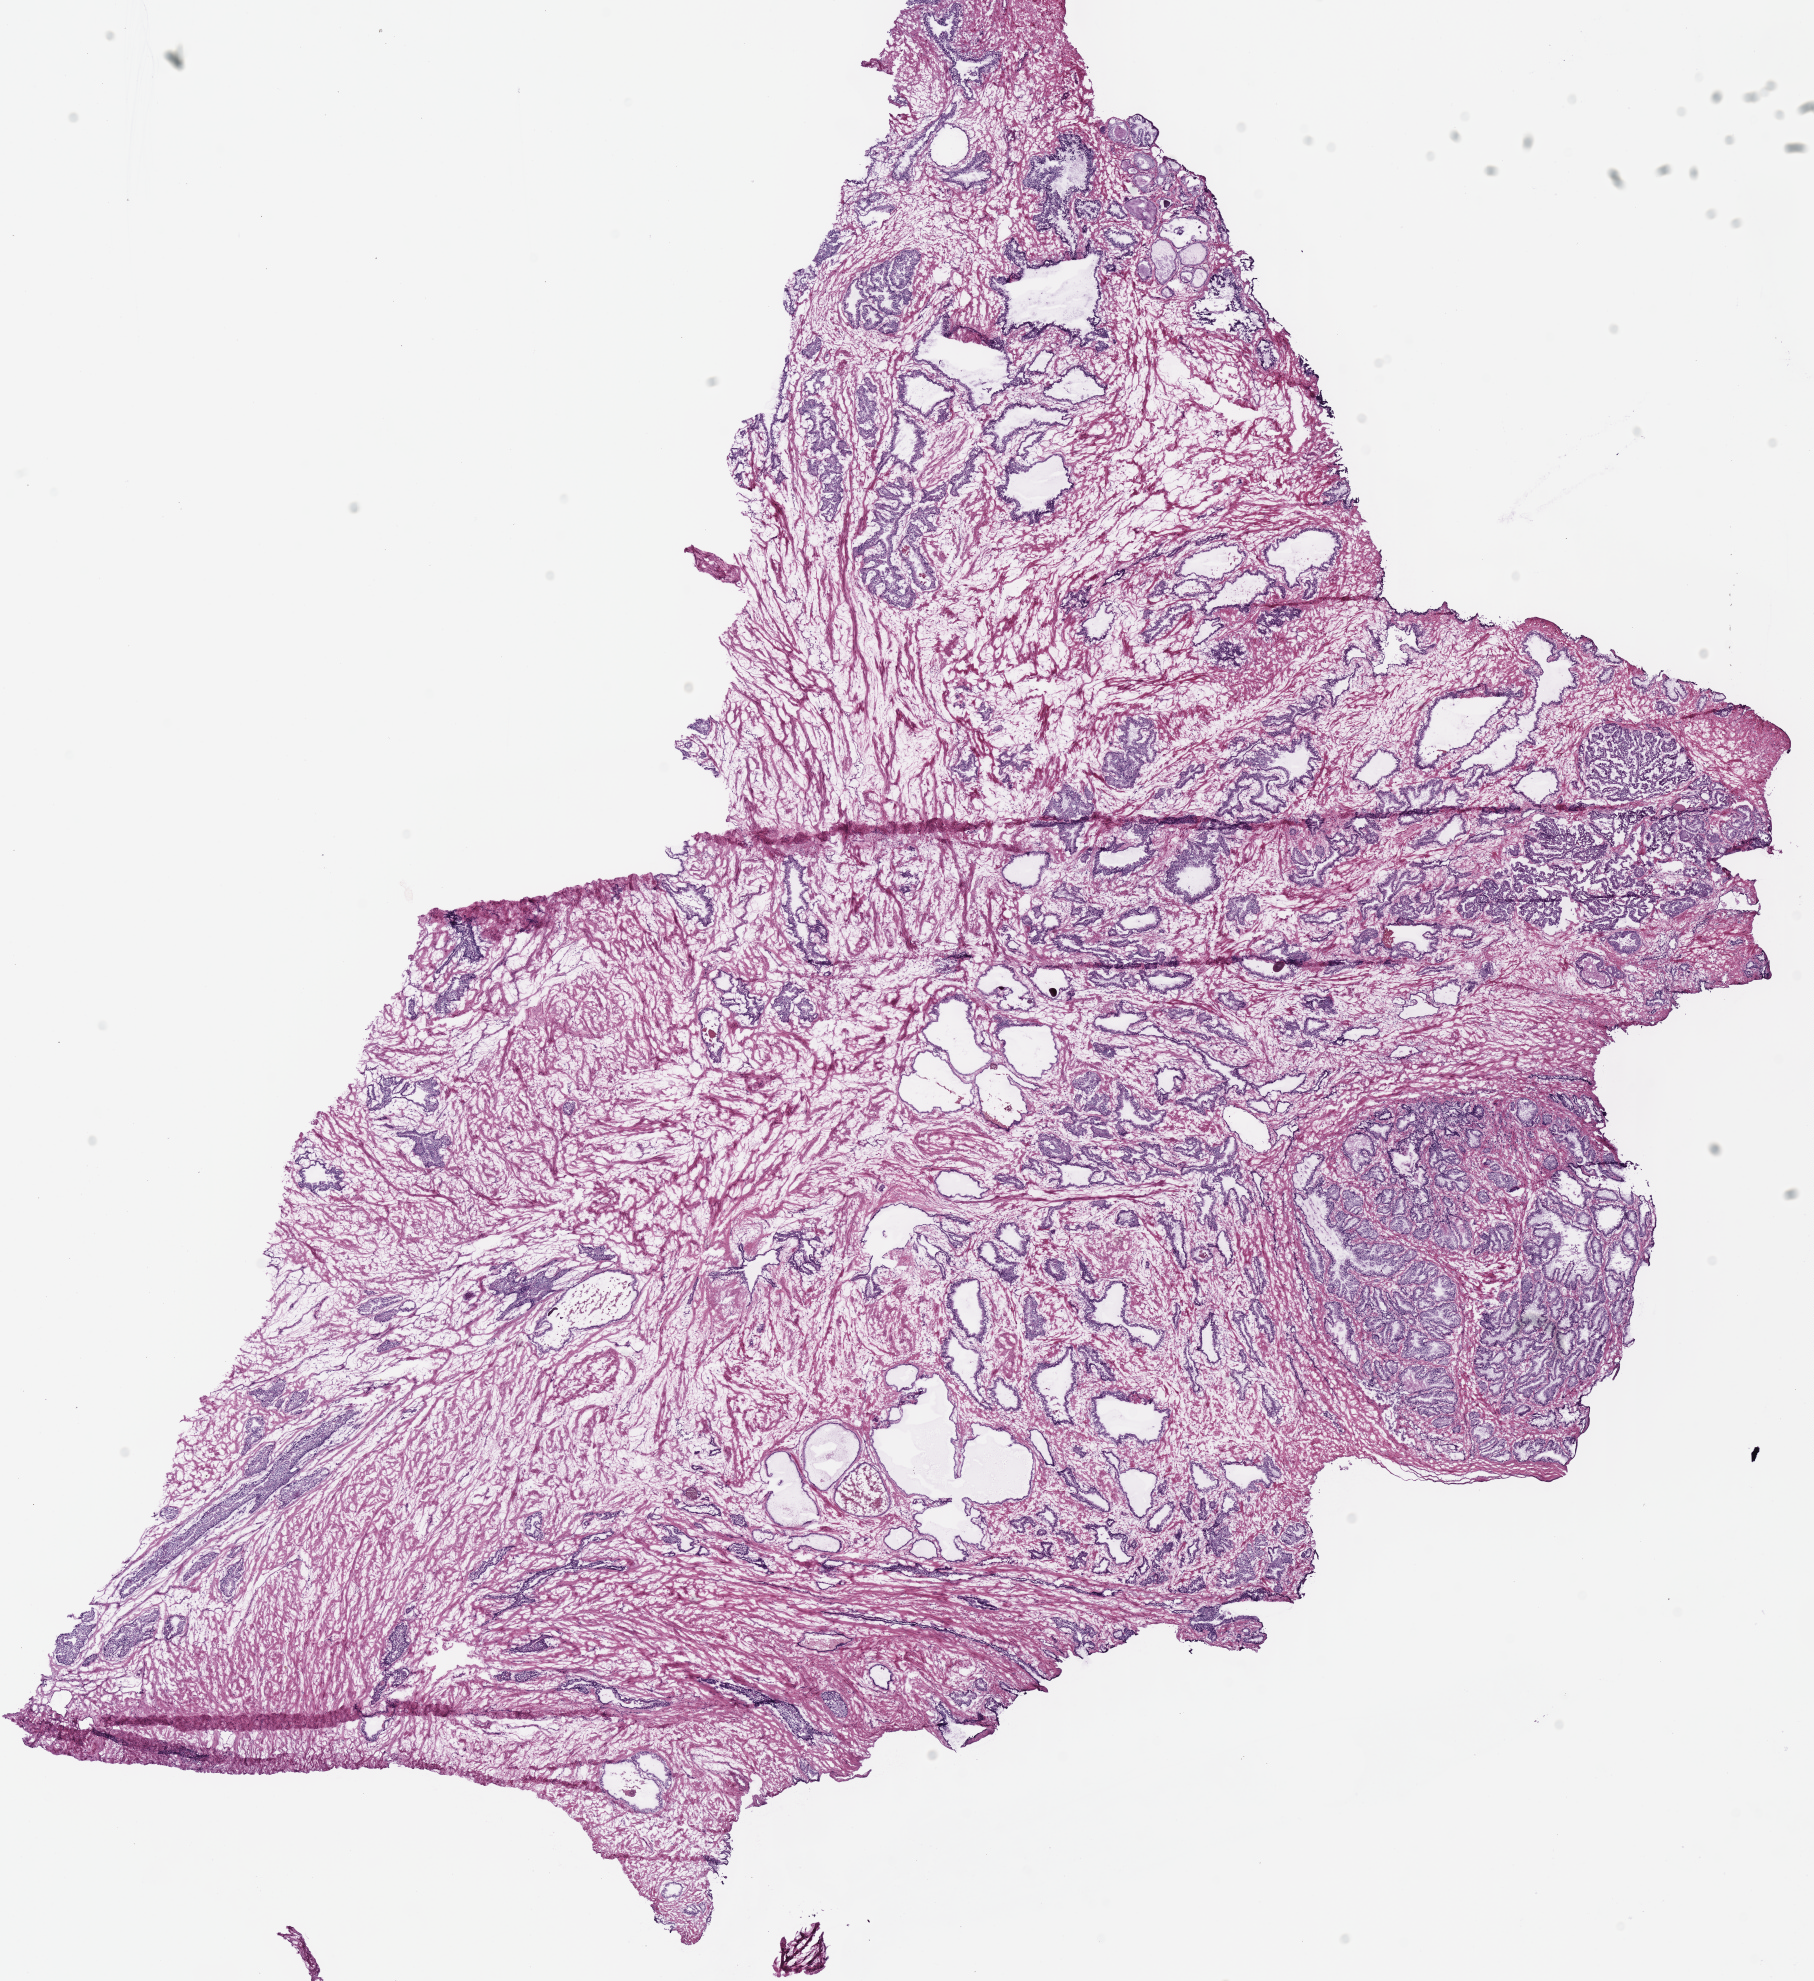
Whole-slide histology image, H&E-stained, whole scanned area (about 14.3 x 15.6 mm, from a 40x scan) shown as a low-resolution overview, frozen section from the top of the tissue portion, solid tissue normal (non-tumour tissue) sample from the prostate. Male, age 71 years at initial diagnosis.
* this section: solid tissue normal (non-tumour) sample from the same patient
* patient diagnosis: Acinar cell carcinoma (prostate gland)